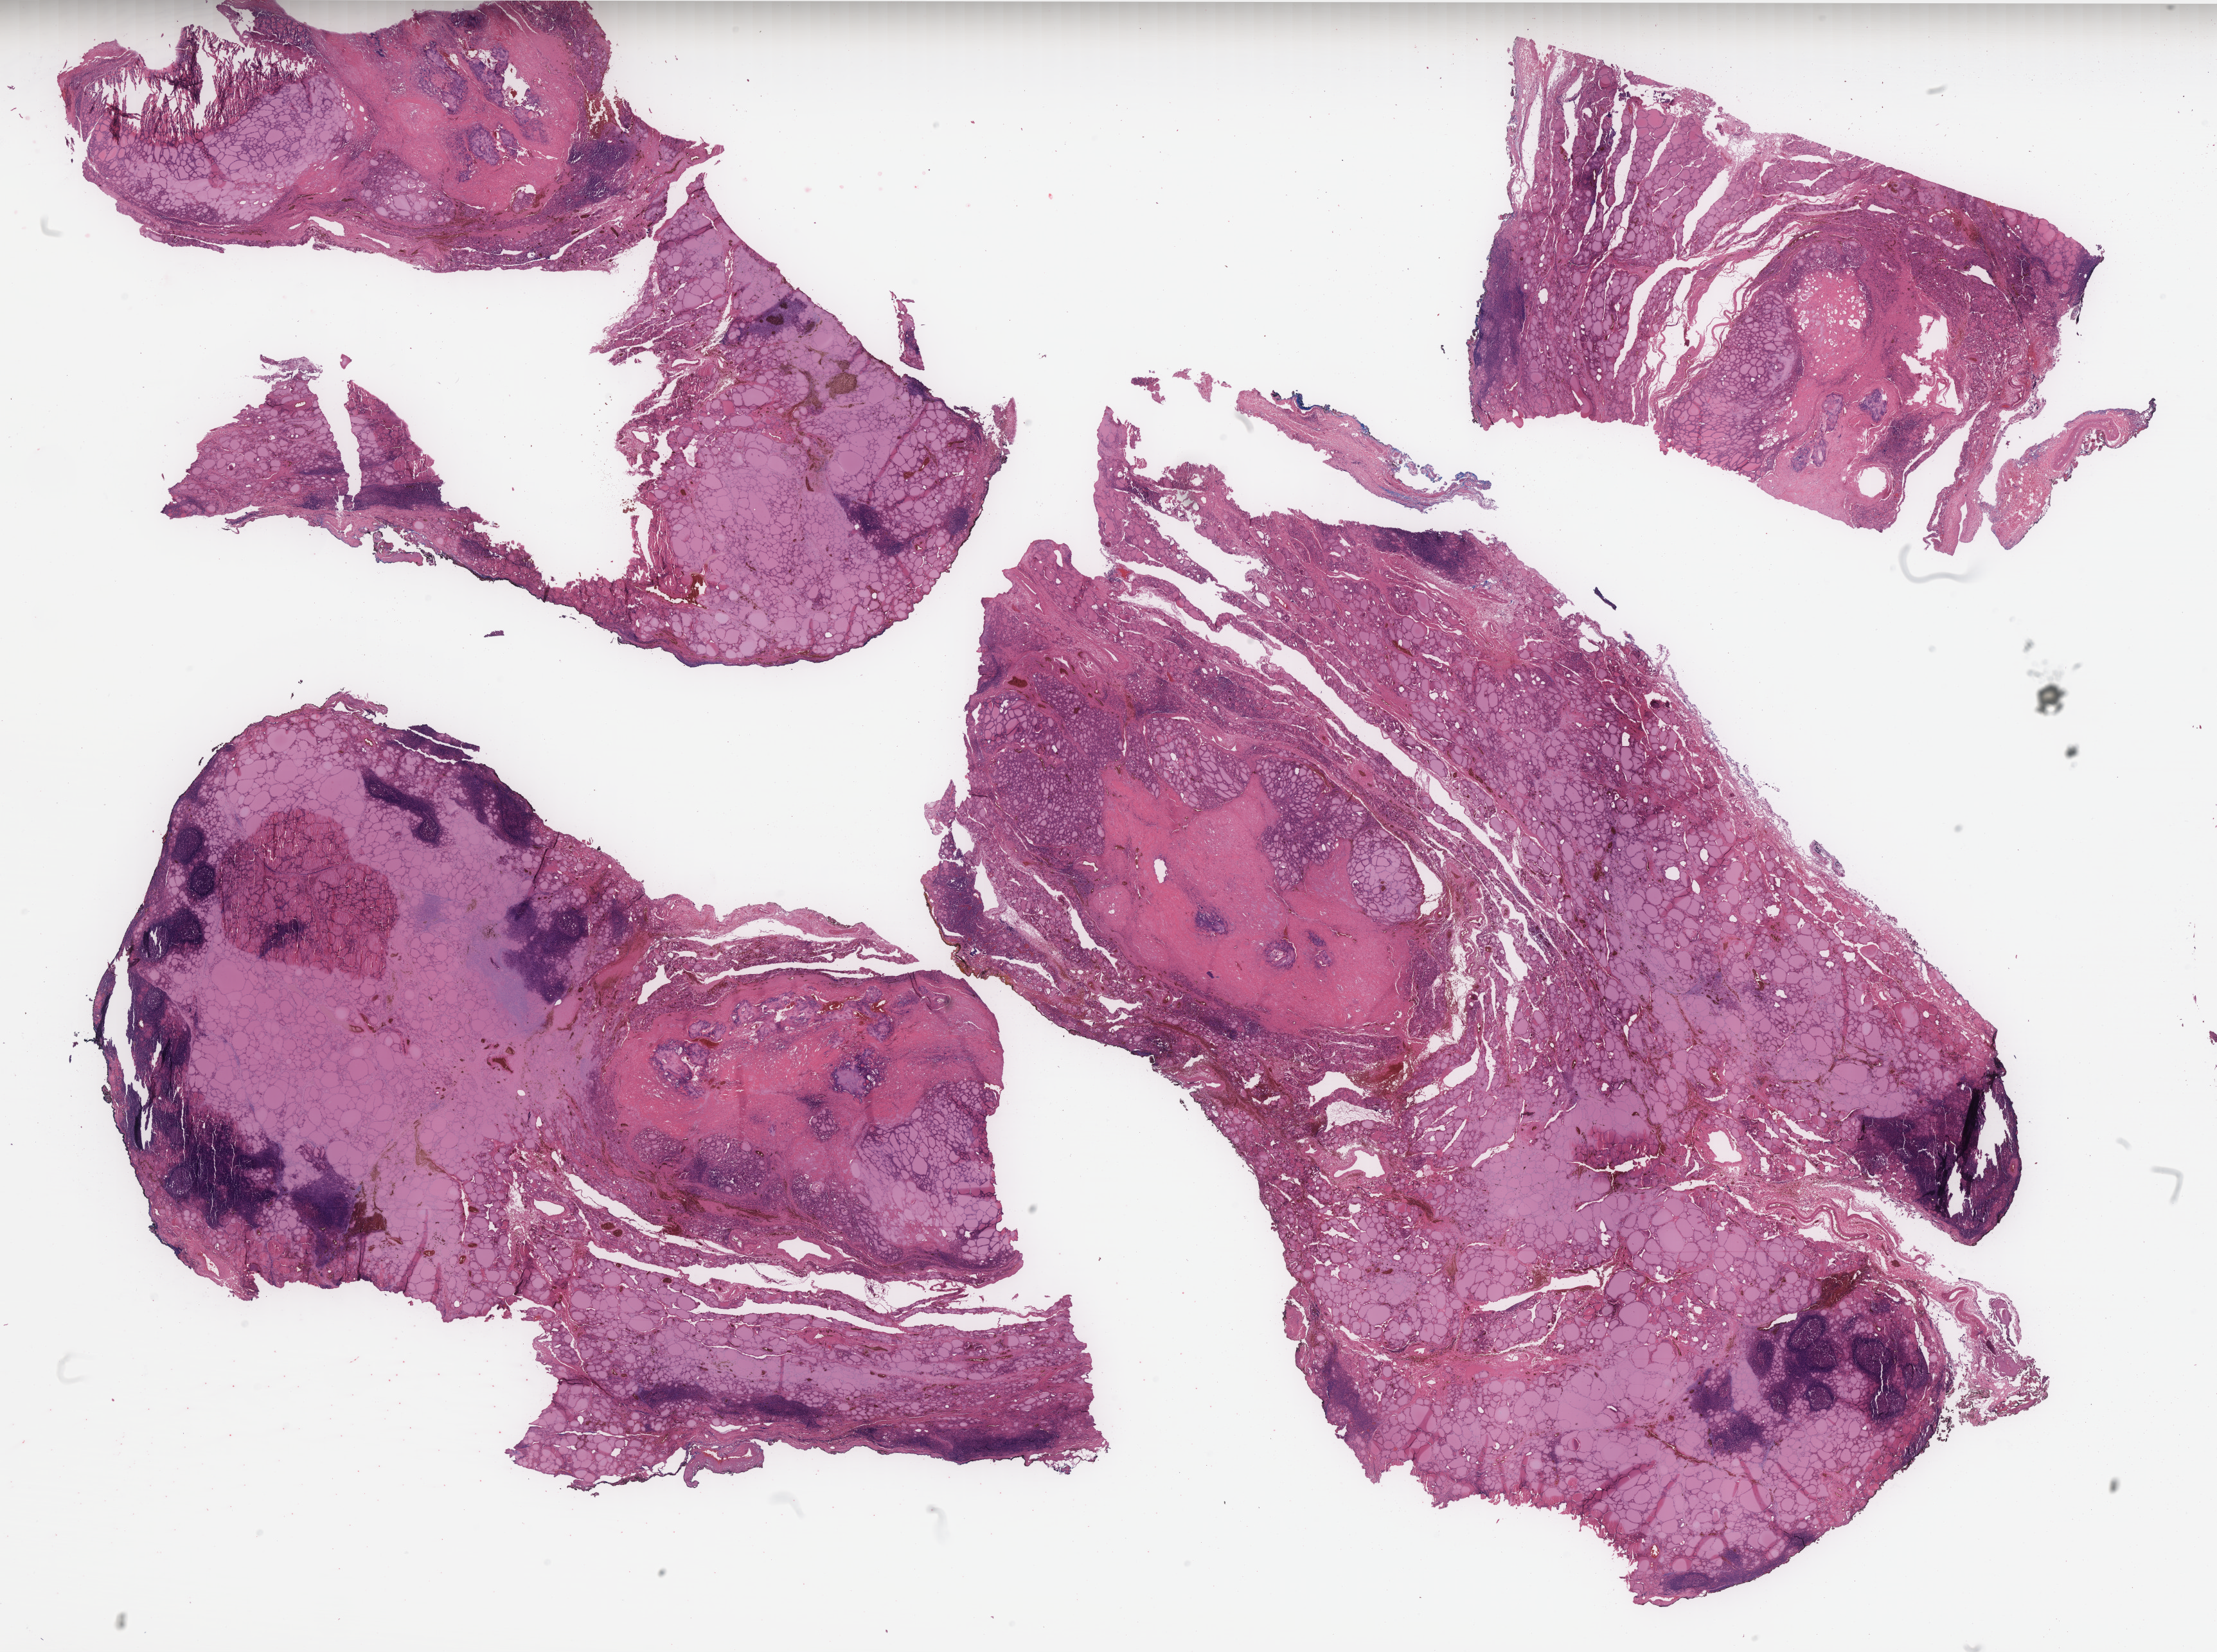
H&E-stained whole-slide image — low-resolution overview of the scanned area, about 27.7 x 20.6 mm. Formalin-fixed paraffin-embedded (FFPE) diagnostic section. Sample: primary tumour, thyroid. Female, age 33 years at initial diagnosis.
• AJCC pathologic stage: I (7th edition)
• lymph nodes positive (case pathology): 0 of 3 examined
• pathologic diagnosis: Papillary adenocarcinoma, NOS